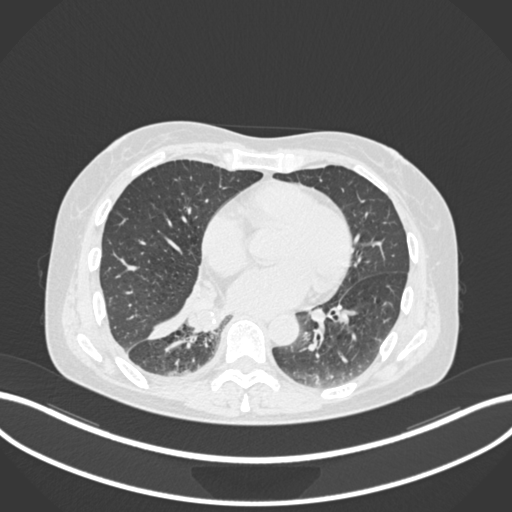
Chest CT, one axial slice; slice 65 of 168 in the series (ordered by position); reconstruction kernel B30f; 120 kVp; lung window (W 1500 / L -600 HU); 1 mm slice thickness; 512 × 512 image matrix, field of view 400 × 400 mm. Patient: female, 63 years. From the clinical record (not read from this slice): clinical TNM (as recorded): T1c N0 M0.
Structures marked on this image (rectangle marked by the reading radiologist):
- lung tumour (recorded histology: adenocarcinoma): bounding box (x1, y1, x2, y2) in pixels: (189, 296, 224, 339)